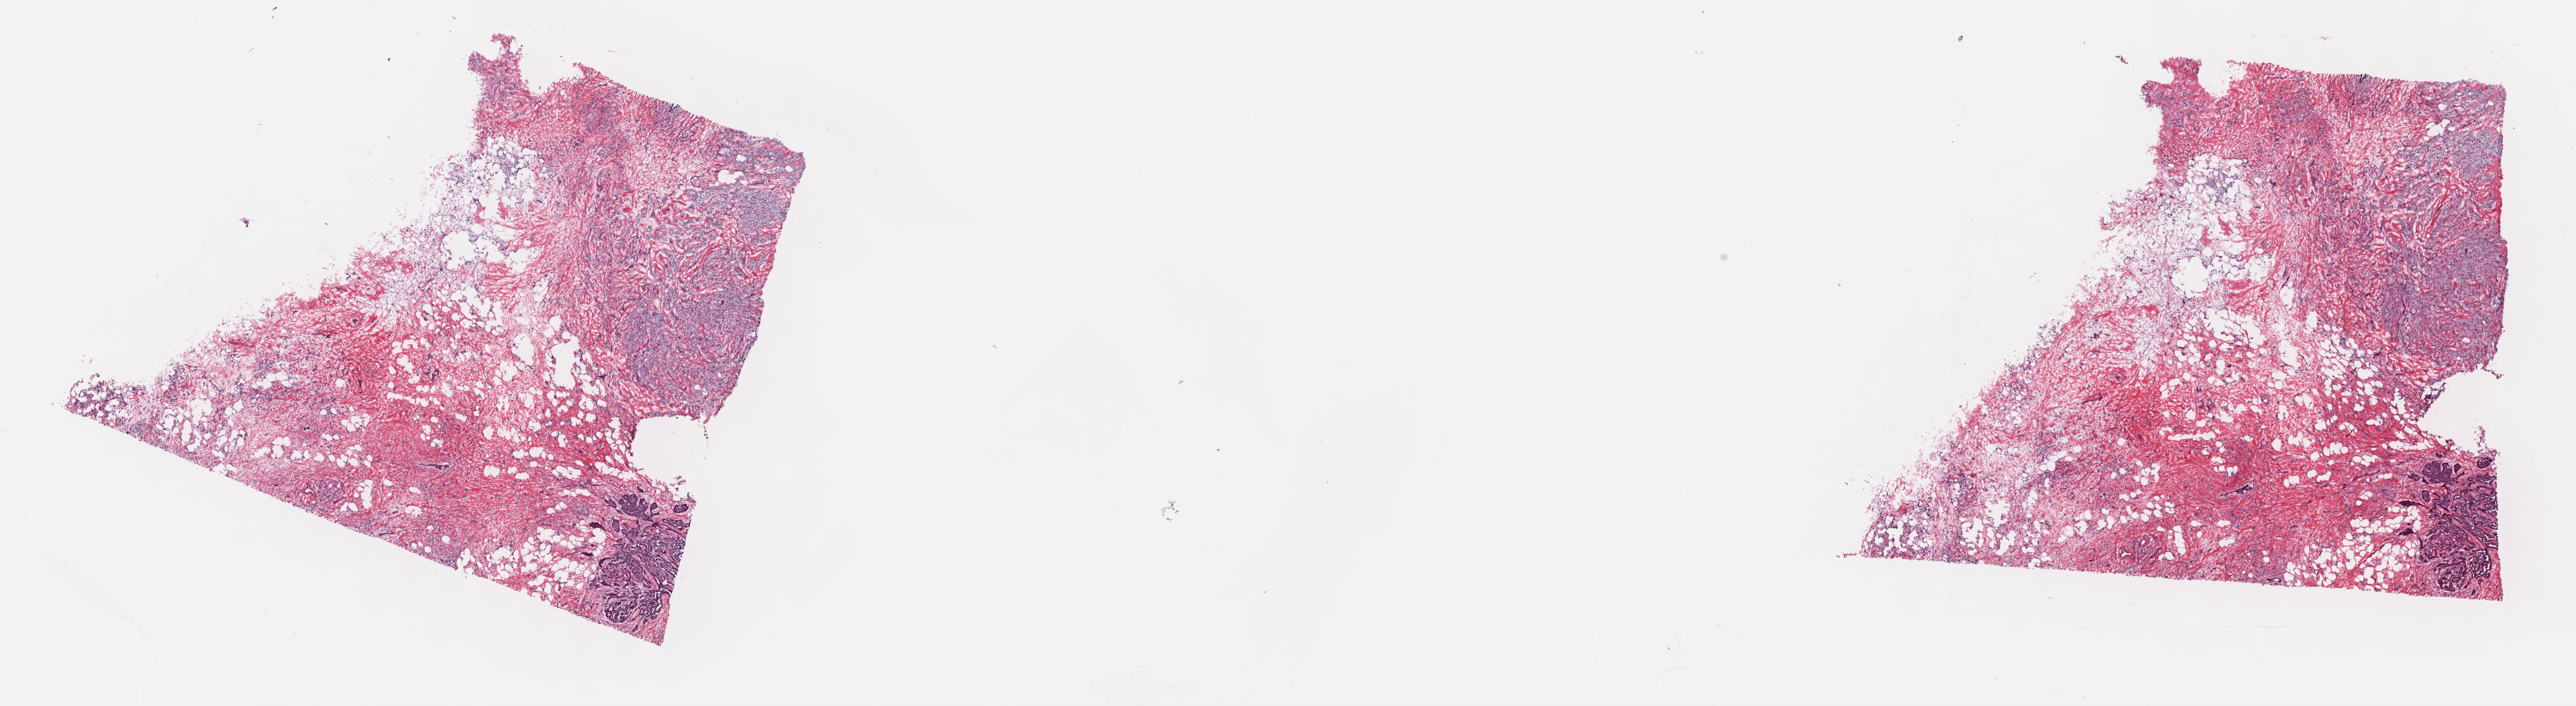
Digitized H&E tissue section (whole slide) — shown as a low-resolution overview of the whole scanned area (about 30.2 x 8.3 mm); frozen section; breast, primary tumour sample. Patient: female, age at initial diagnosis 79 years. Composition of this section per pathologist review: tumour cells 60%, tumour nuclei 60%, normal cells 0%, stromal cells 40%, necrosis 0%. Inflammatory infiltration, as recorded: lymphocyte infiltration 40%, monocyte infiltration 20%, neutrophil infiltration 20%.
* TNM: T3 N3a M0
* laterality: right
* pathologic diagnosis: Infiltrating lobular mixed with other types of carcinoma
* AJCC pathologic stage: IIIC